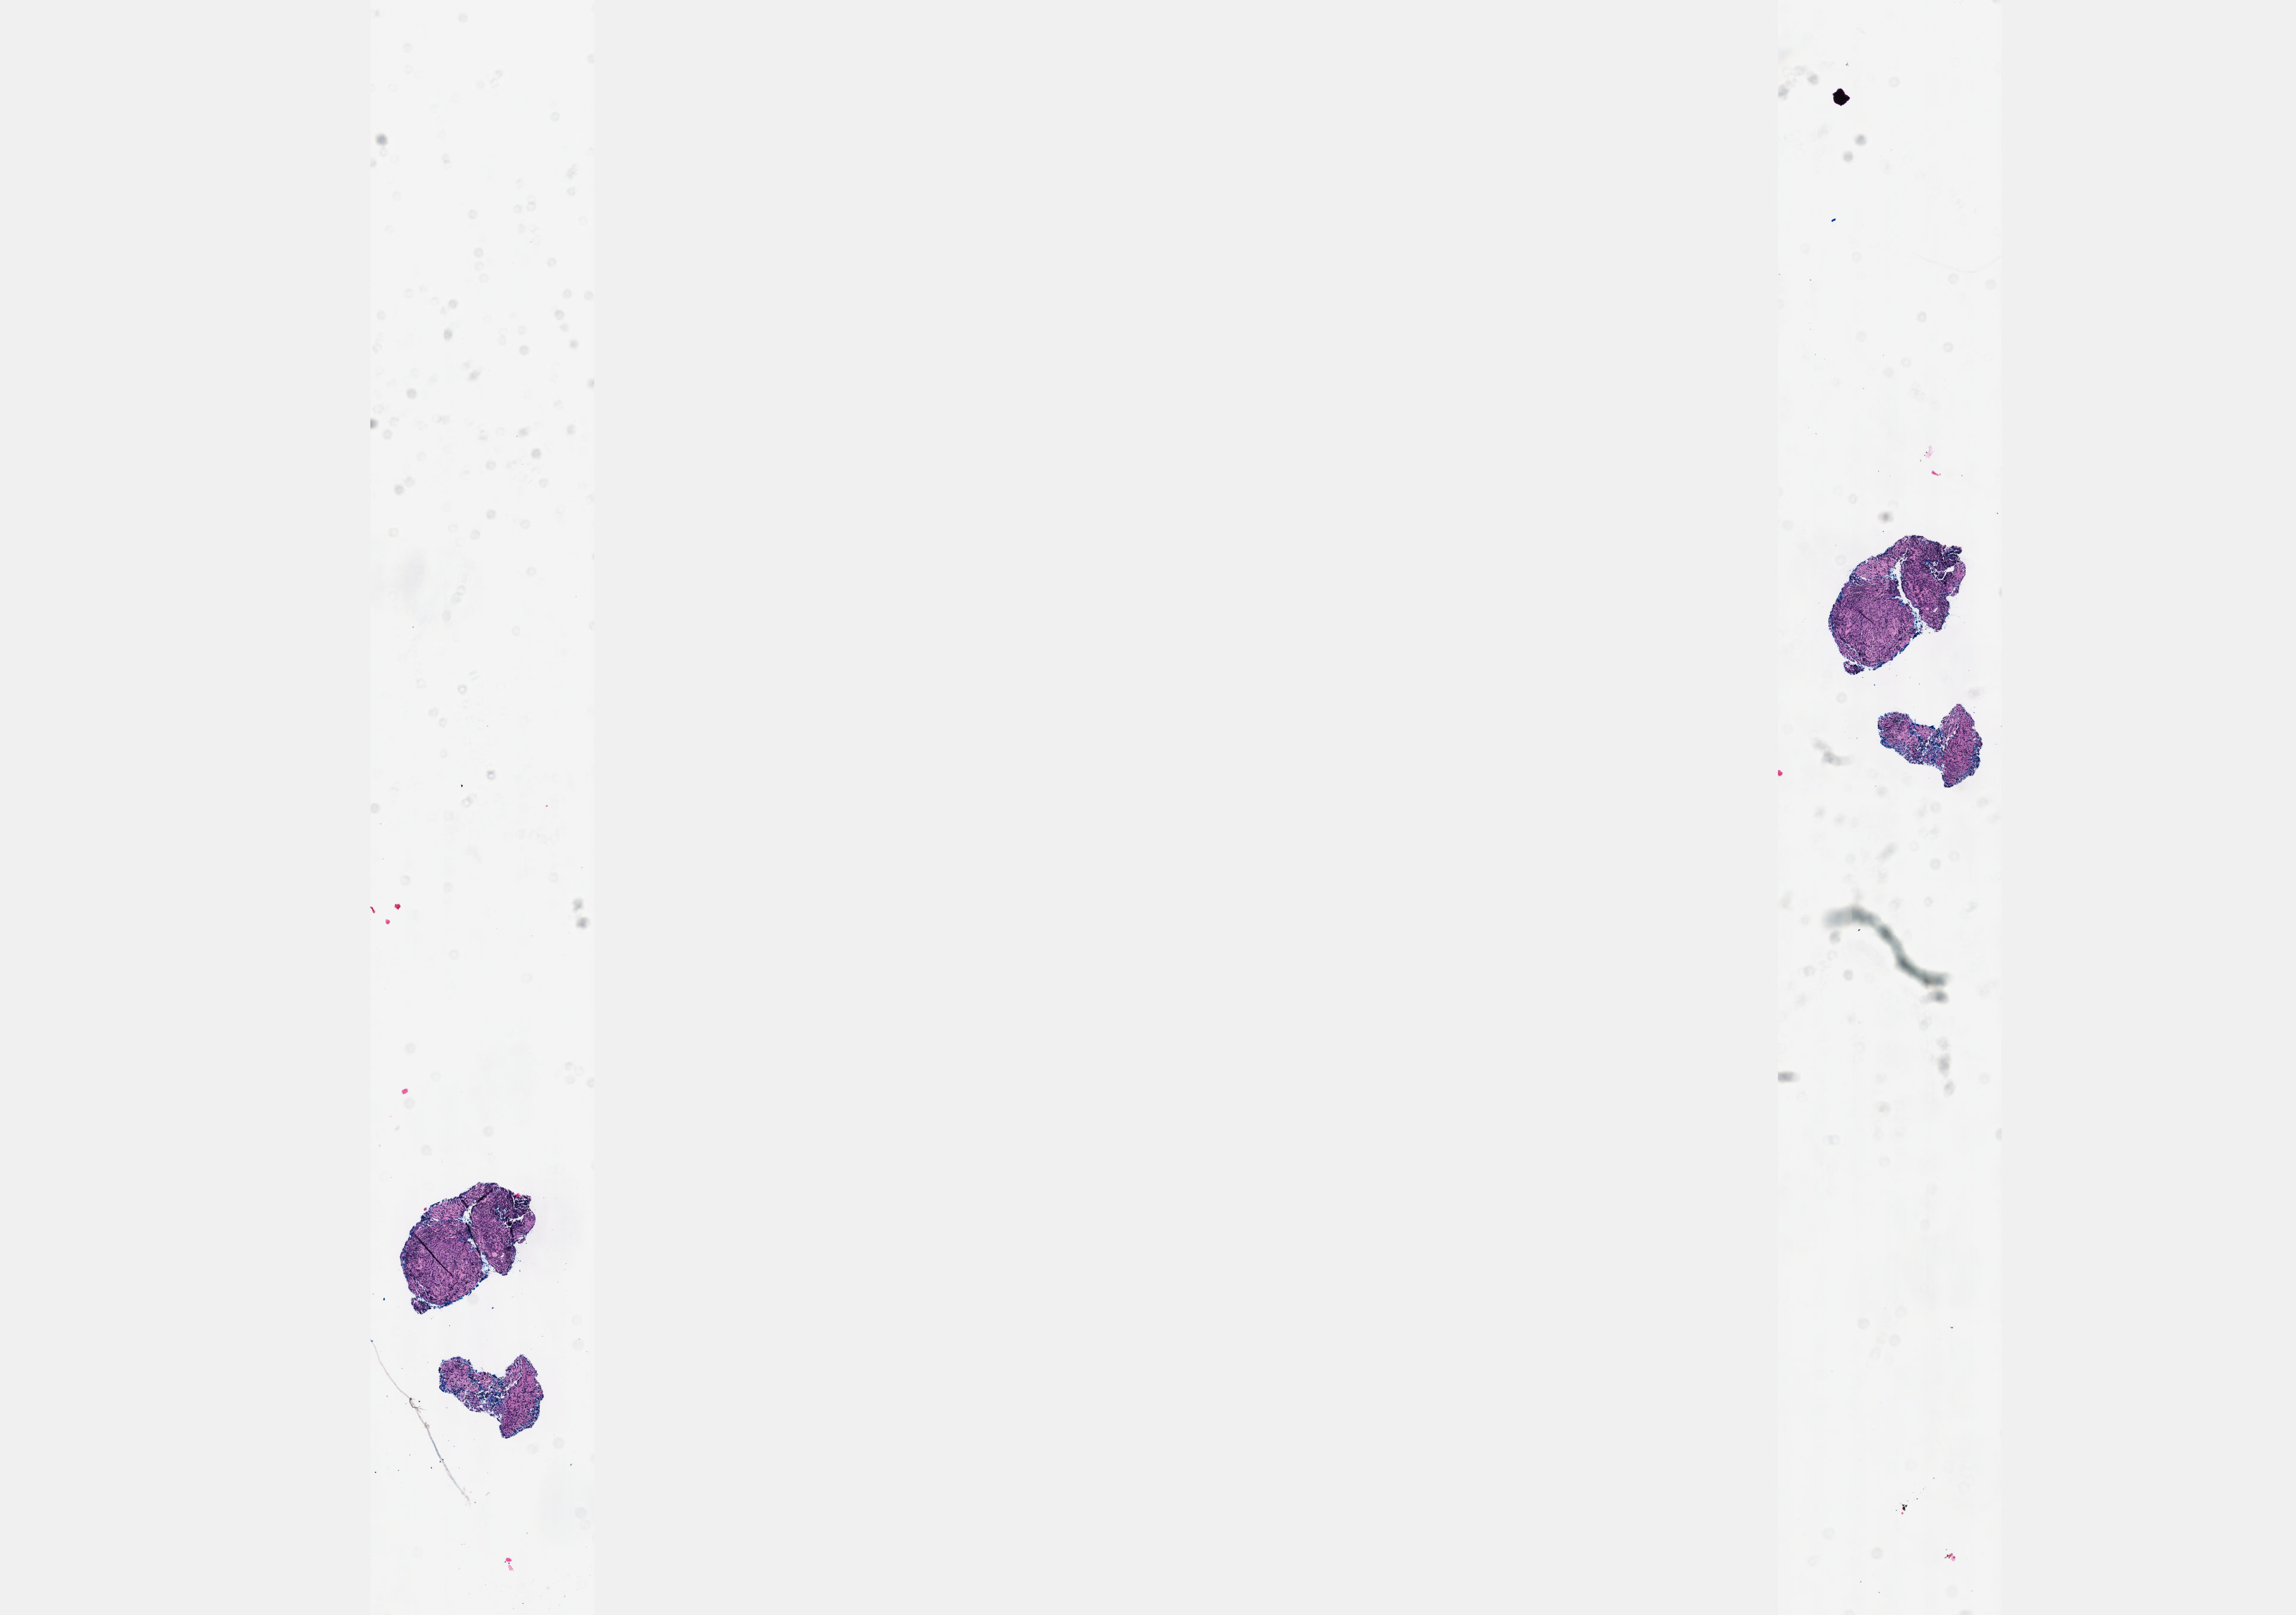
Whole-slide histology image, H&E-stained, a low-resolution overview of the entire scanned area, about 15.6 x 11.0 mm, formalin-fixed paraffin-embedded (FFPE) diagnostic section, sample: primary tumour, lymphoid tissue. Female, age 60 years at initial diagnosis.
Pathologic diagnosis: Diffuse large B-cell lymphoma, NOS (thyroid gland).